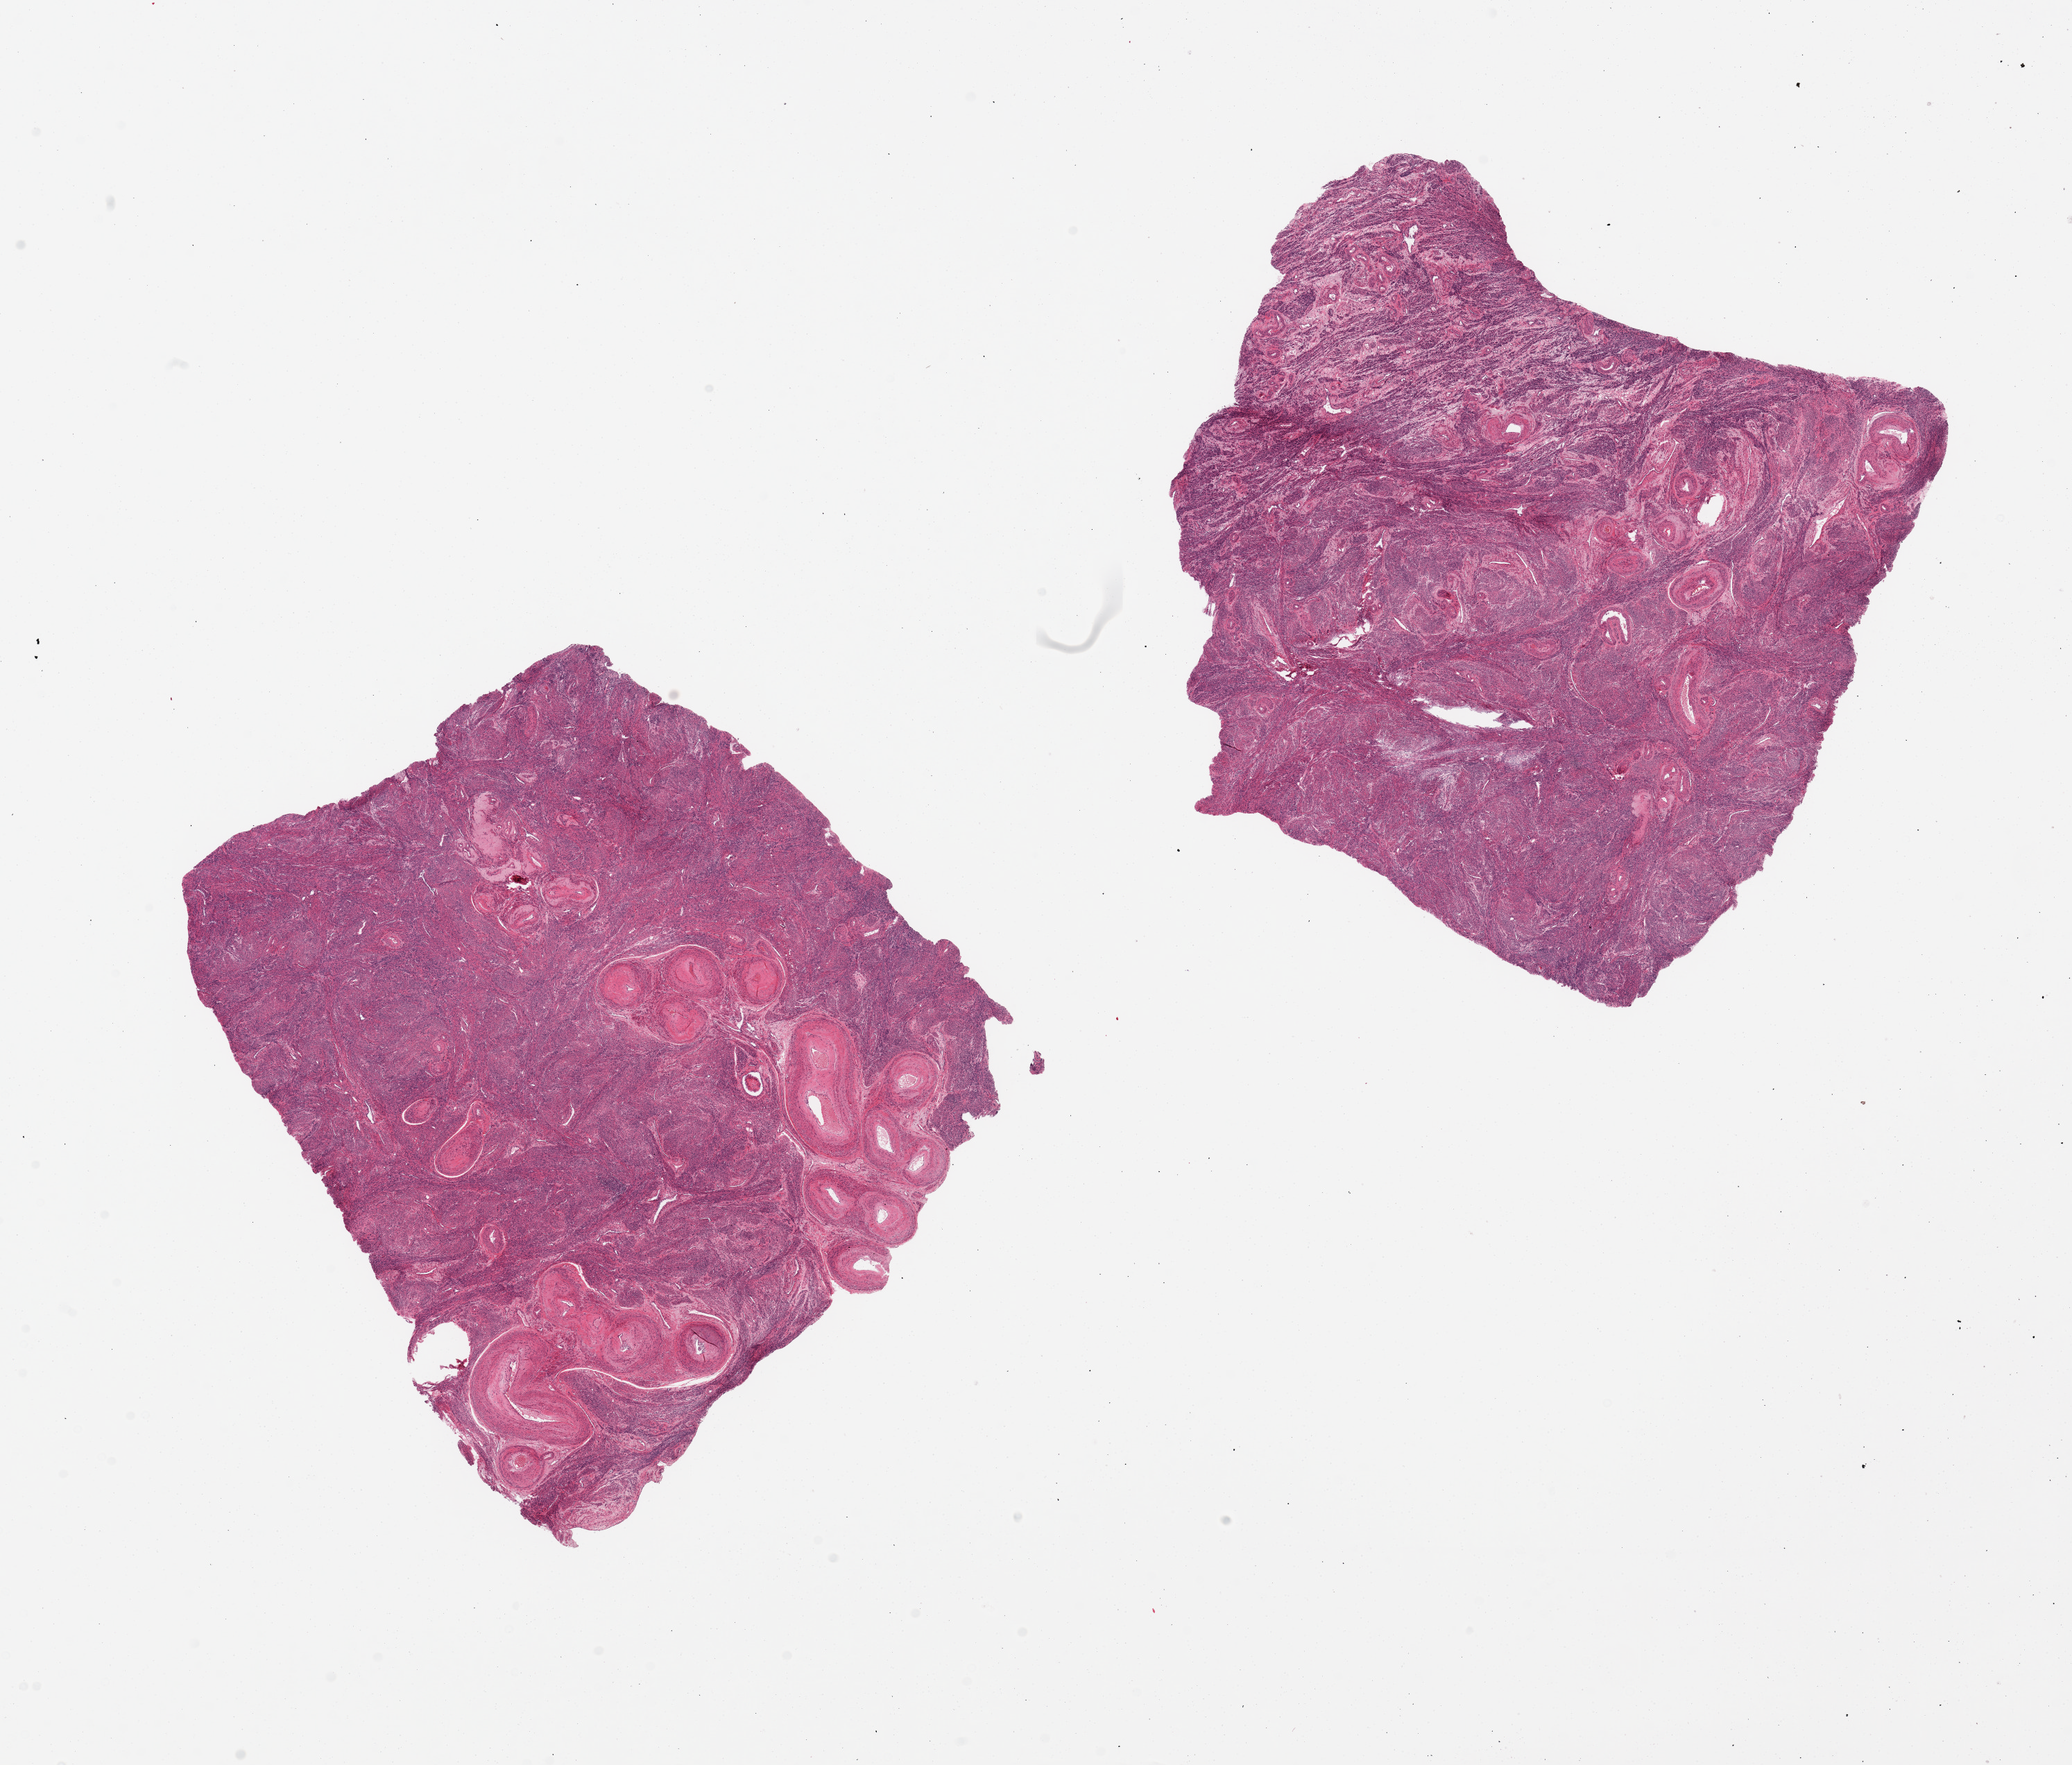
Whole-slide image, hematoxylin and eosin (H&E) stain, brightfield, a low-resolution overview of the entire scanned area, about 23.6 x 20.1 mm, PAXgene-fixed paraffin-embedded (PFPE) section, section of uterus (target tissue), tissue donor sample.
Reviewer comment on this tissue sample: 2 pieces, 9x8 and 8x8mm. All myometrium in these cuts, no endometrium.